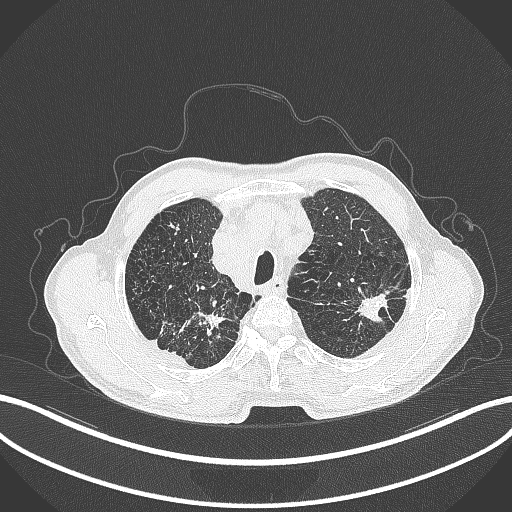
Chest CT, one axial slice. Slice 368 of 463 in the series (ordered by position). 120 kVp. Lung window (W 1500 / L -600 HU). 1 mm slice thickness. 512 × 512 image matrix. Male patient, age 74 years. Case-level facts recorded for this patient, not image findings: clinical TNM (as recorded): T2a N1 M0.
Structures marked on this image (rectangle marked by the reading radiologist):
- lung tumour (recorded histology: adenocarcinoma): bounding box [x1, y1, x2, y2] px = [351, 289, 394, 325]